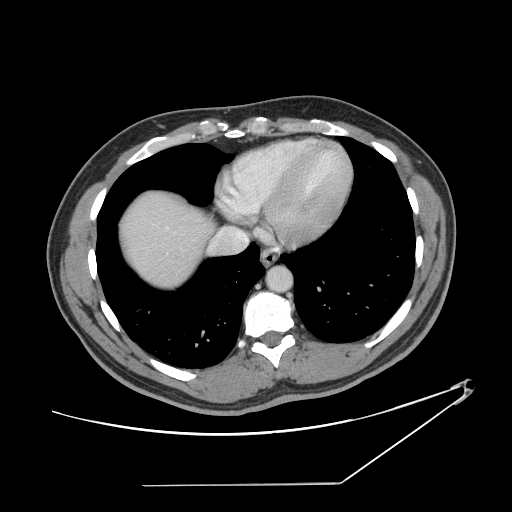
Contrast-enhanced abdominal CT, one axial slice; position 136 of 152 along the scan axis; reconstruction kernel STANDARD; intravenous contrast given; soft-tissue window (W 400 / L 40 HU); 512 × 512 image matrix, field of view 432 × 432 mm. Male patient, age 45 years. Case-level facts recorded for this patient, not image findings: diagnosis: colorectal cancer liver metastases, imaged before liver resection; multiple liver metastases: no; largest metastasis: 1 cm; disease in both lobes: no.
Outlined on this slice (outlined manually by an expert reader):
- hepatic veins: bounding box <167,227,248,244> (left, top, right, bottom; pixels)
- liver: <121,193,211,287>
- planned liver remnant (the part of the liver to remain after resection): <122,193,211,287>